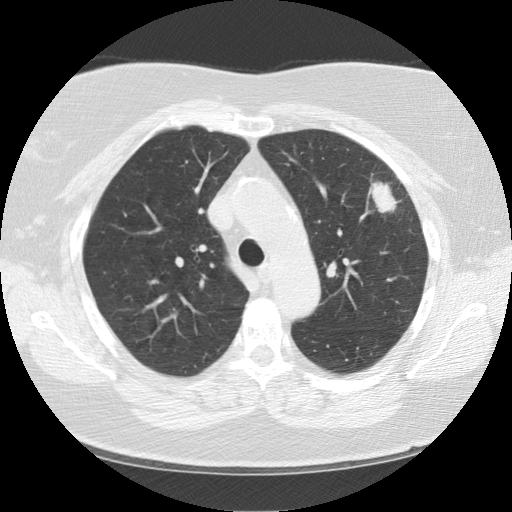
Chest CT (low-dose screening protocol), one axial image. Baseline annual screen. Lung window (W 1500 / L -600 HU). Standard (soft-tissue) reconstruction kernel (STANDARD). Female, age 67 years at enrolment. Former smoker at enrolment.
Lesion marked by an expert reader, bounding box (x1, y1, x2, y2) in pixels: (346, 156, 422, 229). Reader record for this screening exam (exam-level; its link to the box is not recorded): non-calcified nodule or mass ≥4 mm, left upper lobe, 28 × 19 mm, soft tissue attenuation. Official screen result: positive, change unspecified: nodule(s) >= 4 mm or enlarging nodule(s), mass(es), or other non-specific abnormalities suspicious for lung cancer. Participant outcome: lung cancer diagnosed 33 days after this screen — squamous cell carcinoma, NOS, left upper lobe, poorly differentiated (G3), stage IA (AJCC 6th edition), 25 mm at pathology.